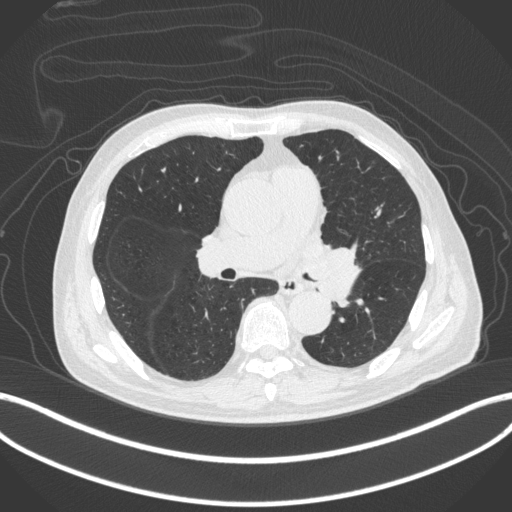
Chest CT, one axial slice. Slice 237 of 420 in the series (ordered by position). Reconstruction kernel B31f. Lung window (W 1500 / L -600 HU). 1 mm slice thickness. 512 × 512 image matrix, field of view 400 × 400 mm. Patient: male, 77 years. Case-level facts recorded for this patient, not image findings: clinical TNM (as recorded): T3 N1 M0.
Annotated regions visible in this slice (bounding box drawn by a radiologist):
- lung tumour (recorded histology: adenocarcinoma): bounding box [x1, y1, x2, y2] px = [305, 242, 366, 307]